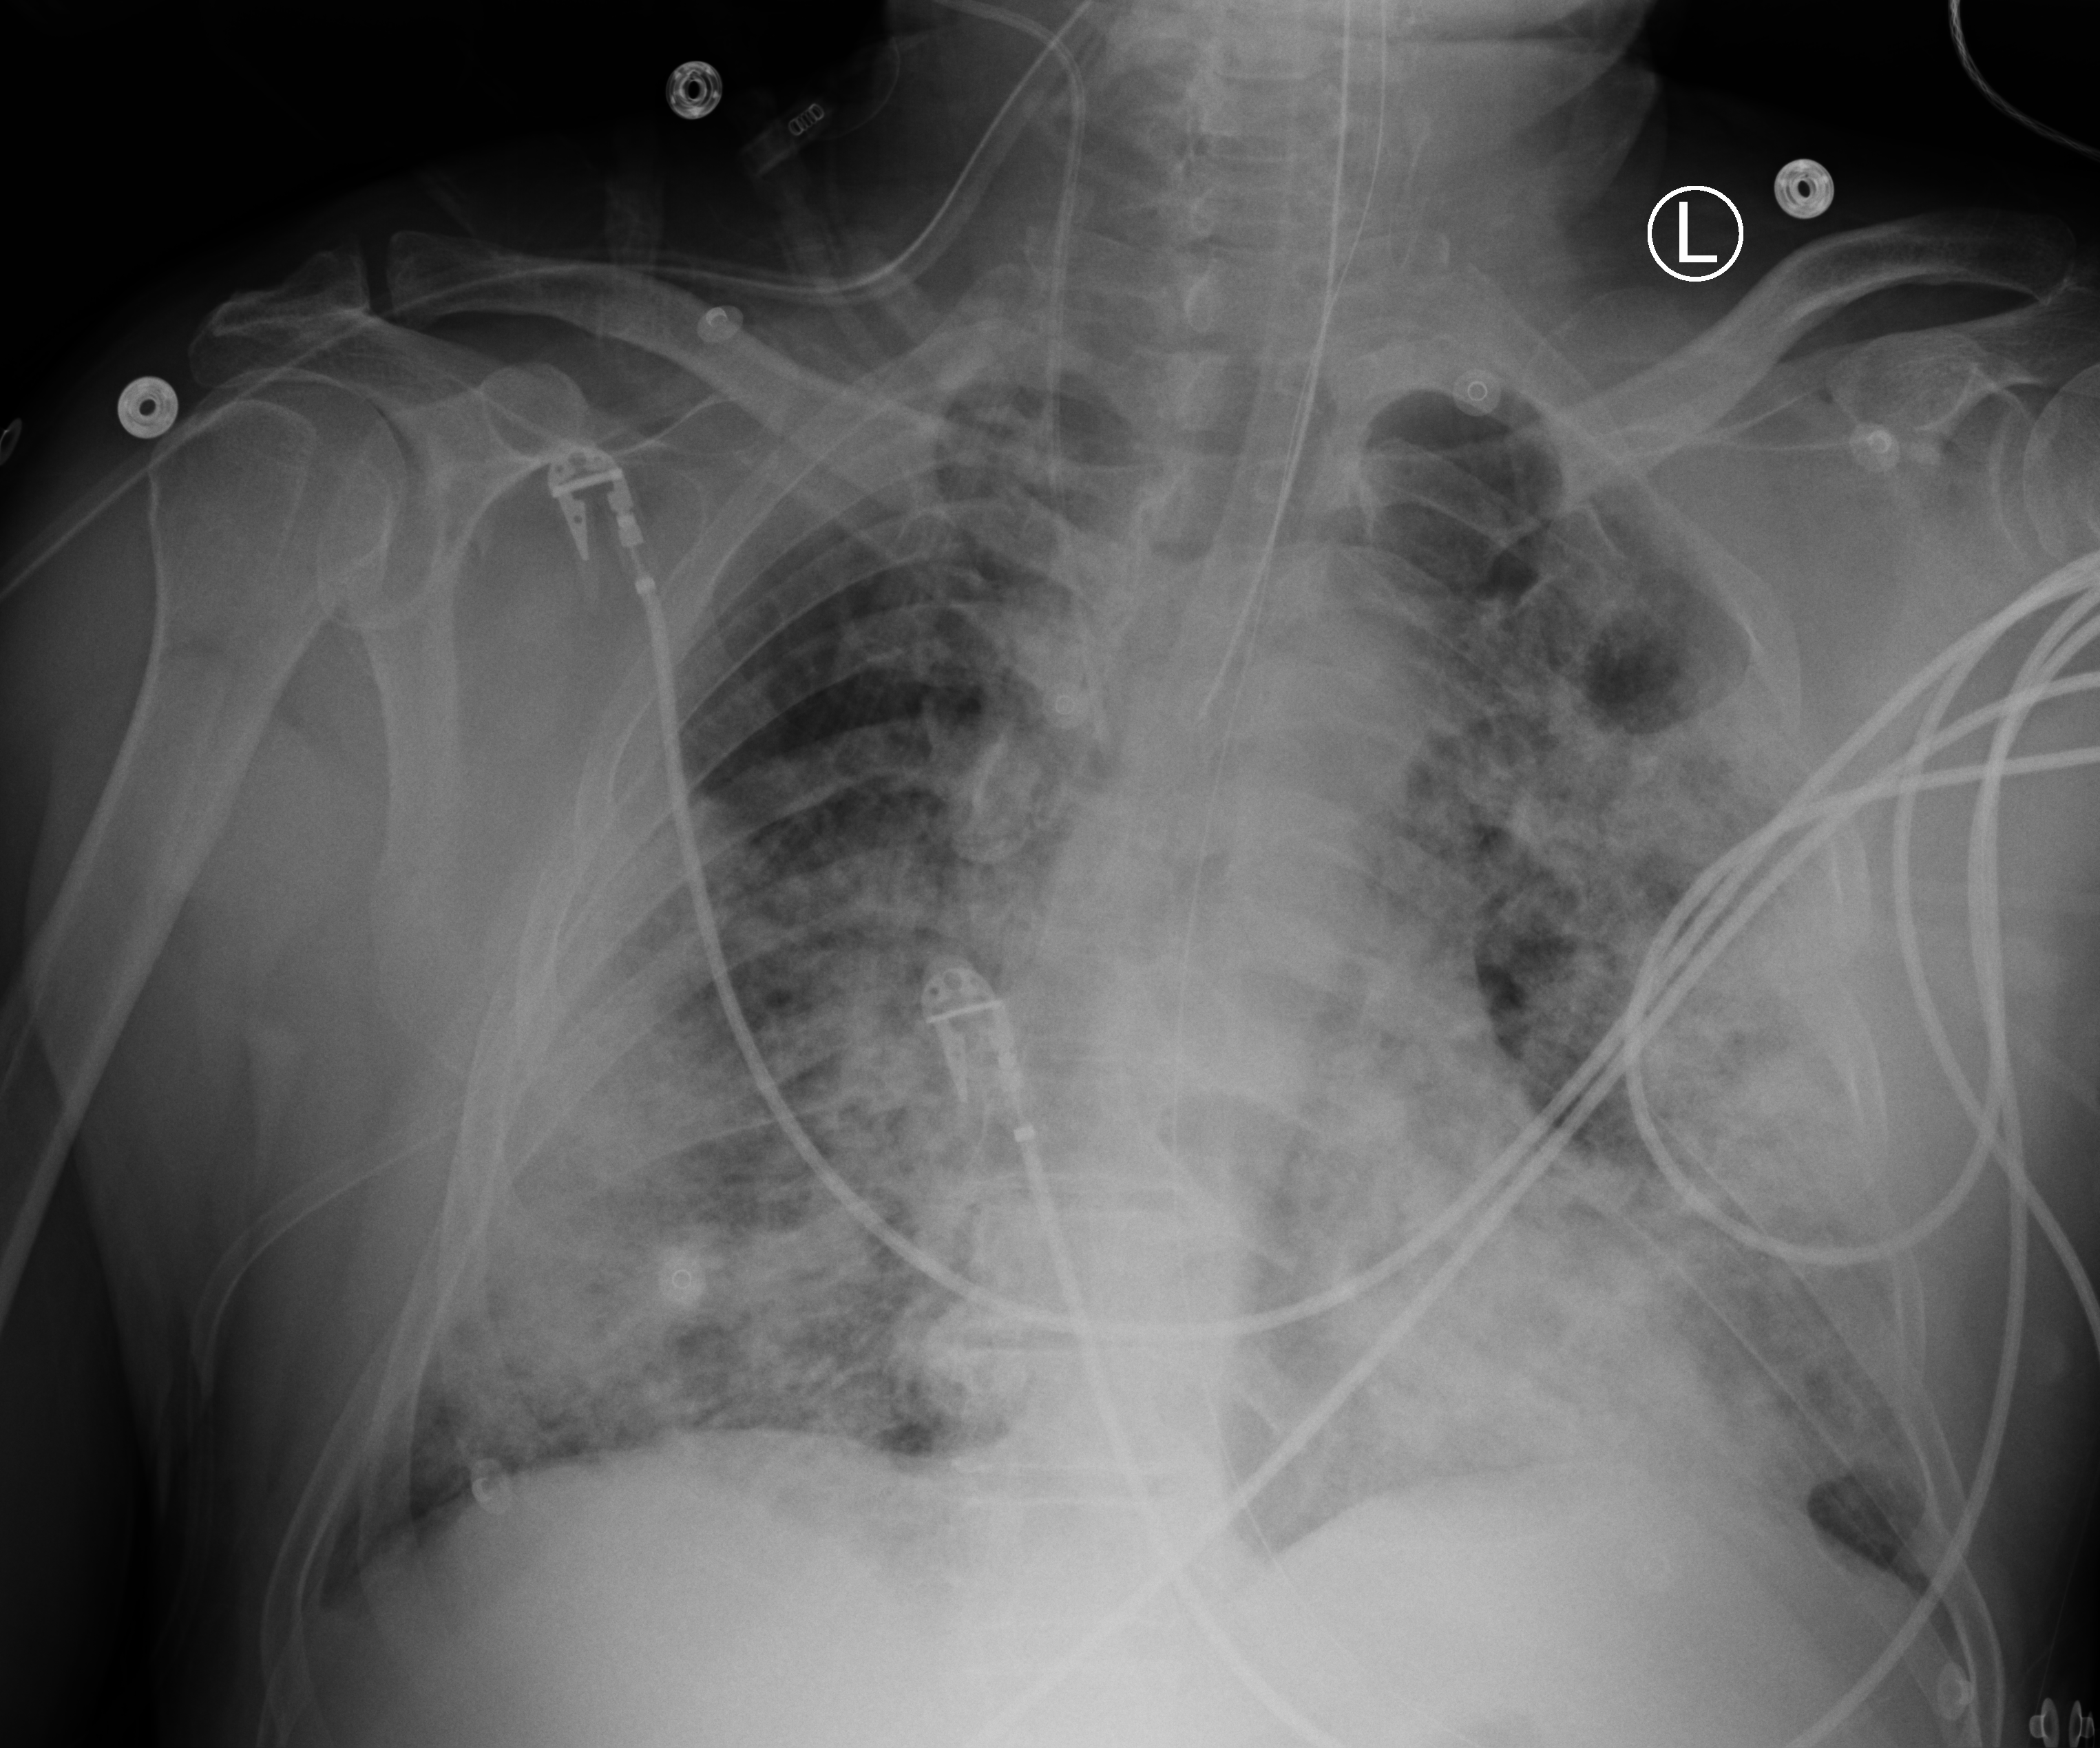
Portable chest radiograph. Patient hospitalised with COVID-19; male, aged 60–74 years.
Hospital-stay facts (about this admission, not read from this image; timing relative to this image not recorded):
- mechanically ventilated during this hospital stay: yes